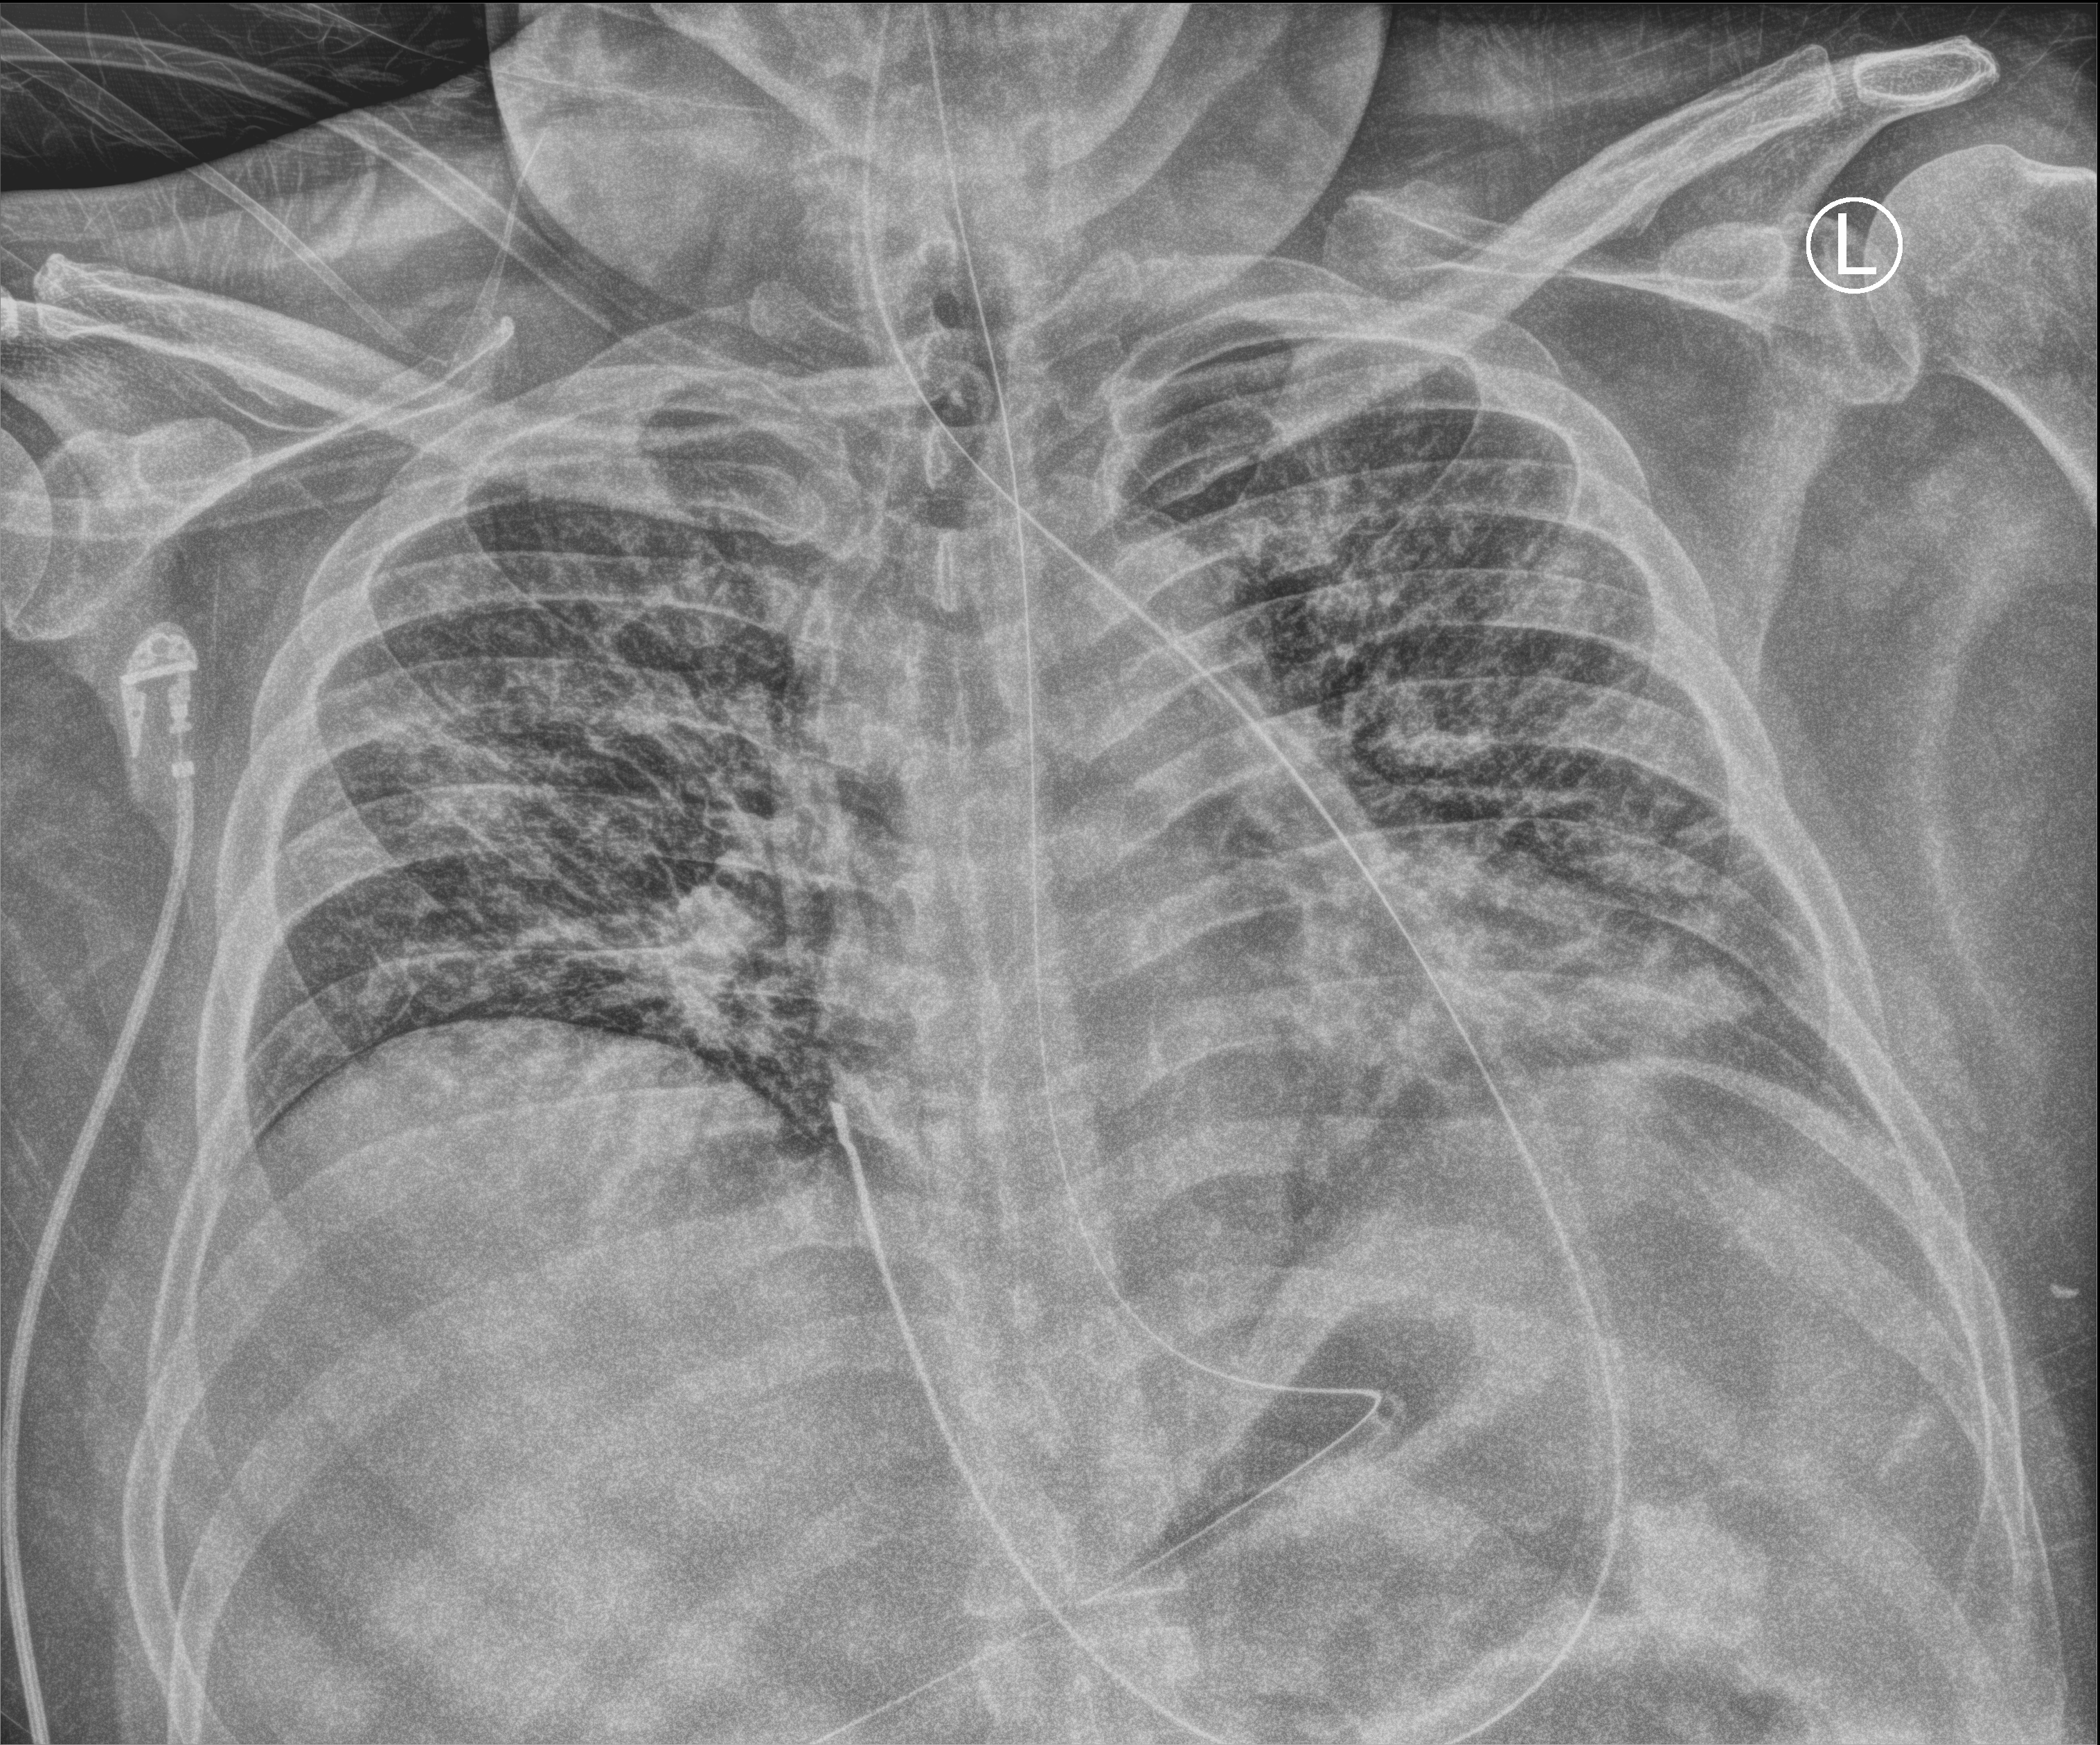
Bedside chest radiograph (computed radiography), anteroposterior (AP) projection. Male patient hospitalised with COVID-19, age 18–59 years.
From the hospital-stay record, not from the radiograph (when in the stay this image was taken is not recorded): mechanically ventilated during this hospital stay: no; other chronic lung disease (admission record): yes.